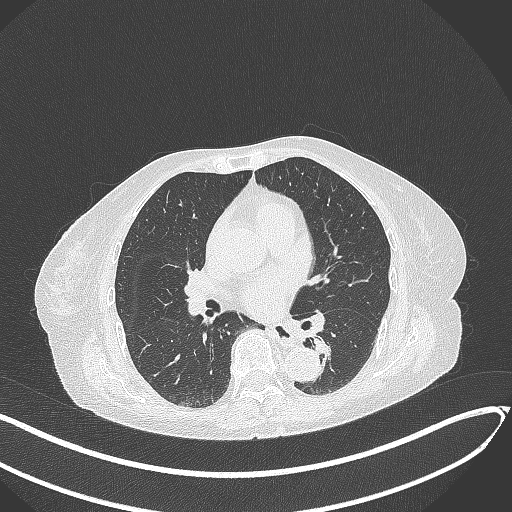
Chest CT, one axial slice; position 130 of 324 along the scan axis; lung window (W 1500 / L -600 HU); 1 mm slice thickness; 512 × 512 image matrix. Female patient, age 82 years. From the clinical record (not read from this slice): clinical TNM (as recorded): T1b N0 M1.
Structures marked on this image (rectangle marked by the reading radiologist):
- lung tumour (recorded histology: adenocarcinoma): bounding box (x1, y1, x2, y2) in pixels: (308, 336, 336, 364)